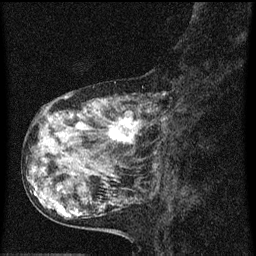
Breast MRI (dynamic contrast-enhanced), one sagittal slice. Dynamic contrast-enhanced series, image 2 of 3 at this slice position (ordered by acquisition). 1.5 T. TE 4.2 ms, TR 8 ms. 2 mm slice thickness. 256 × 256 image matrix, field of view 180 × 180 mm. Female patient, age 55 years.
Outlined on this slice (semi-automatic segmentation, software-assisted and operator-edited):
- analysis volume of interest (the breast-tissue region the enhancement analysis was run in; not a lesion): box from (x=38, y=92) to (x=173, y=159) px
- tumour enhancement mask (voxels above the 70 % enhancement threshold inside the analysis volume of interest): (x=66, y=96)–(x=159, y=145)